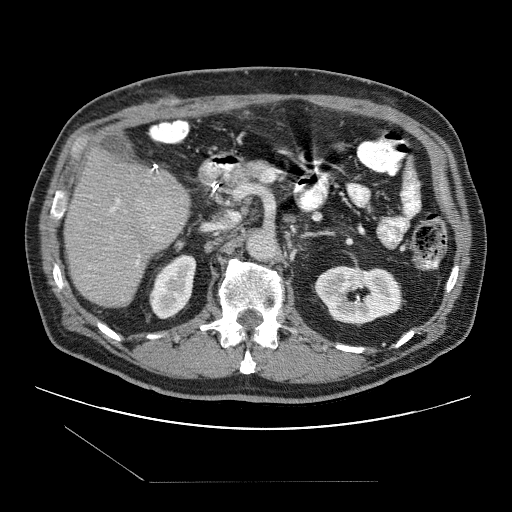
Contrast-enhanced abdominal CT (liver protocol), one axial slice; slice 42 of 109 in the series (ordered by position); 120 kVp; one of 2 acquisitions stored at this slice position; soft-tissue window (W 400 / L 40 HU); 512 × 512 image matrix, field of view 400 × 400 mm. From the clinical record (not read from this slice): diagnosis: hepatocellular carcinoma (patient treated with transarterial chemoembolisation; whether this scan precedes or follows treatment is not stated here); TNM stage (as recorded): Stage-IIIB; Child-Pugh class: A; tumour differentiation: well differentiated; tumour nodularity: multinodular.
Annotated regions visible in this slice (semi-automatic segmentation, software-assisted and operator-edited):
- liver parenchyma outside the tumour (the mass and vessels are separate outlines, so this box may not span the whole liver): bounding box (x1, y1, x2, y2) in pixels: (64, 148, 190, 306)
- liver vessels: (110, 167, 156, 265)